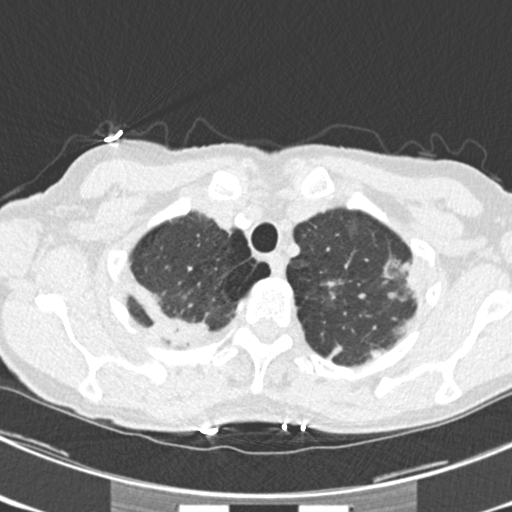
Low-dose screening chest CT, one axial slice; slice 189 of 225 in the series (ordered by position); reconstruction kernel B30f; 120 kVp; lung window (W 1500 / L -600 HU); 512 × 512 image matrix, field of view 302 × 302 mm.
Annotated regions visible in this slice (expert manual segmentation):
- lesion 1 (tumor, upper lobe of left lung): bounding box (x1, y1, x2, y2) in pixels: (402, 263, 413, 287)
- lesion 4 (tumor, upper lobe of right lung): (156, 313, 207, 347)